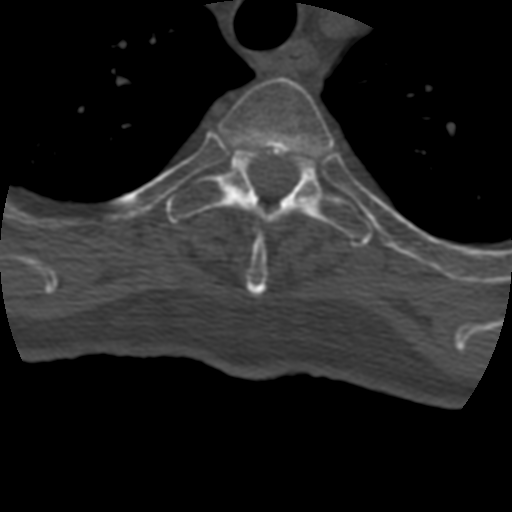
CT including the spine, one axial slice. Slice 343 of 399 in the series (ordered by position). Reconstruction kernel STANDARD. Bone window (W 1800 / L 400 HU). 1.25 mm slice thickness. 512 × 512 image matrix. Patient age 69 years. Case-level facts recorded for this patient, not image findings: primary cancer: prostate.
Outlined on this slice (semi-automatically segmented with operator editing):
- T3 vertebra: bounding box (x1, y1, x2, y2) in pixels: (219, 77, 335, 297)
- T4 vertebra: (167, 149, 374, 247)